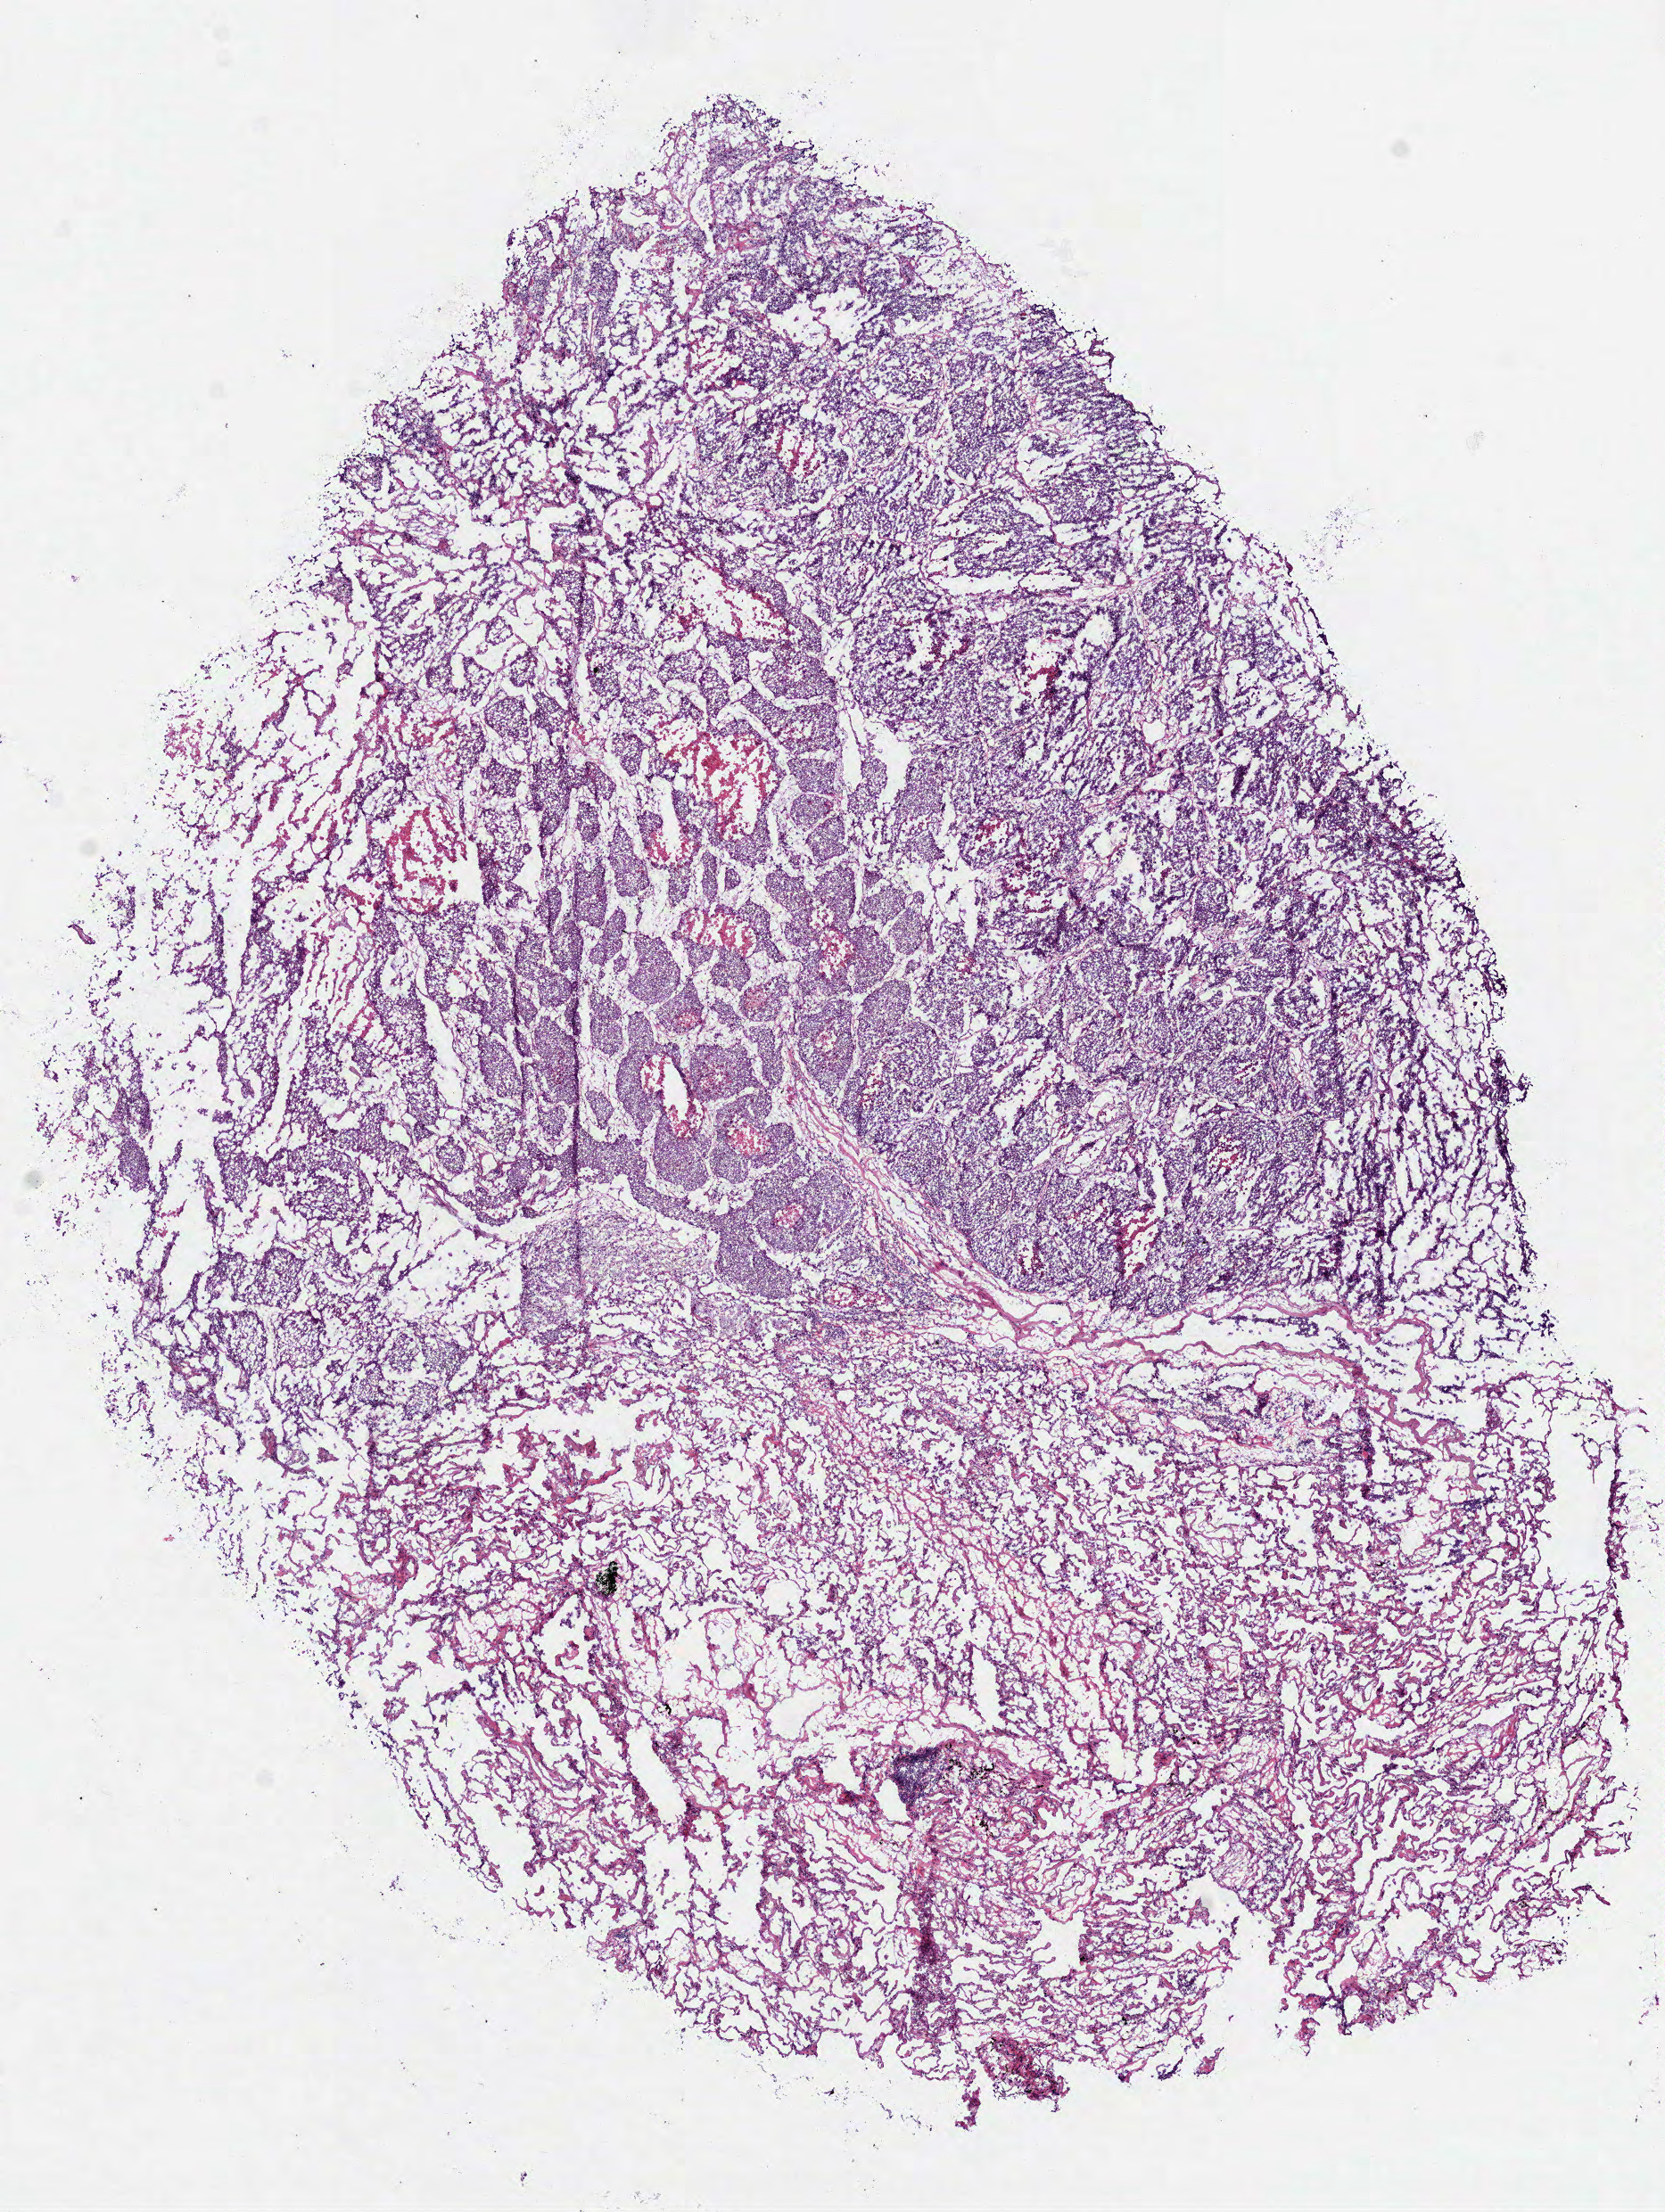
Hematoxylin and eosin (H&E) stained whole-slide image, whole scanned area (about 7.5 x 10.0 mm) shown as a low-resolution overview. Frozen section from the bottom of the tissue portion. Sample: primary tumour, lung. Patient: female, age at initial diagnosis 70 years. Slide review estimates, as recorded: tumour cells 50%, tumour nuclei 70%, normal cells 43%, stromal cells 0%, necrosis 7%. Infiltration values recorded for this section: lymphocyte infiltration 2%, monocyte infiltration 15%, neutrophil infiltration 0%.
Laterality: right. AJCC pathologic stage: IA. Histologic diagnosis: Squamous cell carcinoma, NOS (lower lobe, lung).